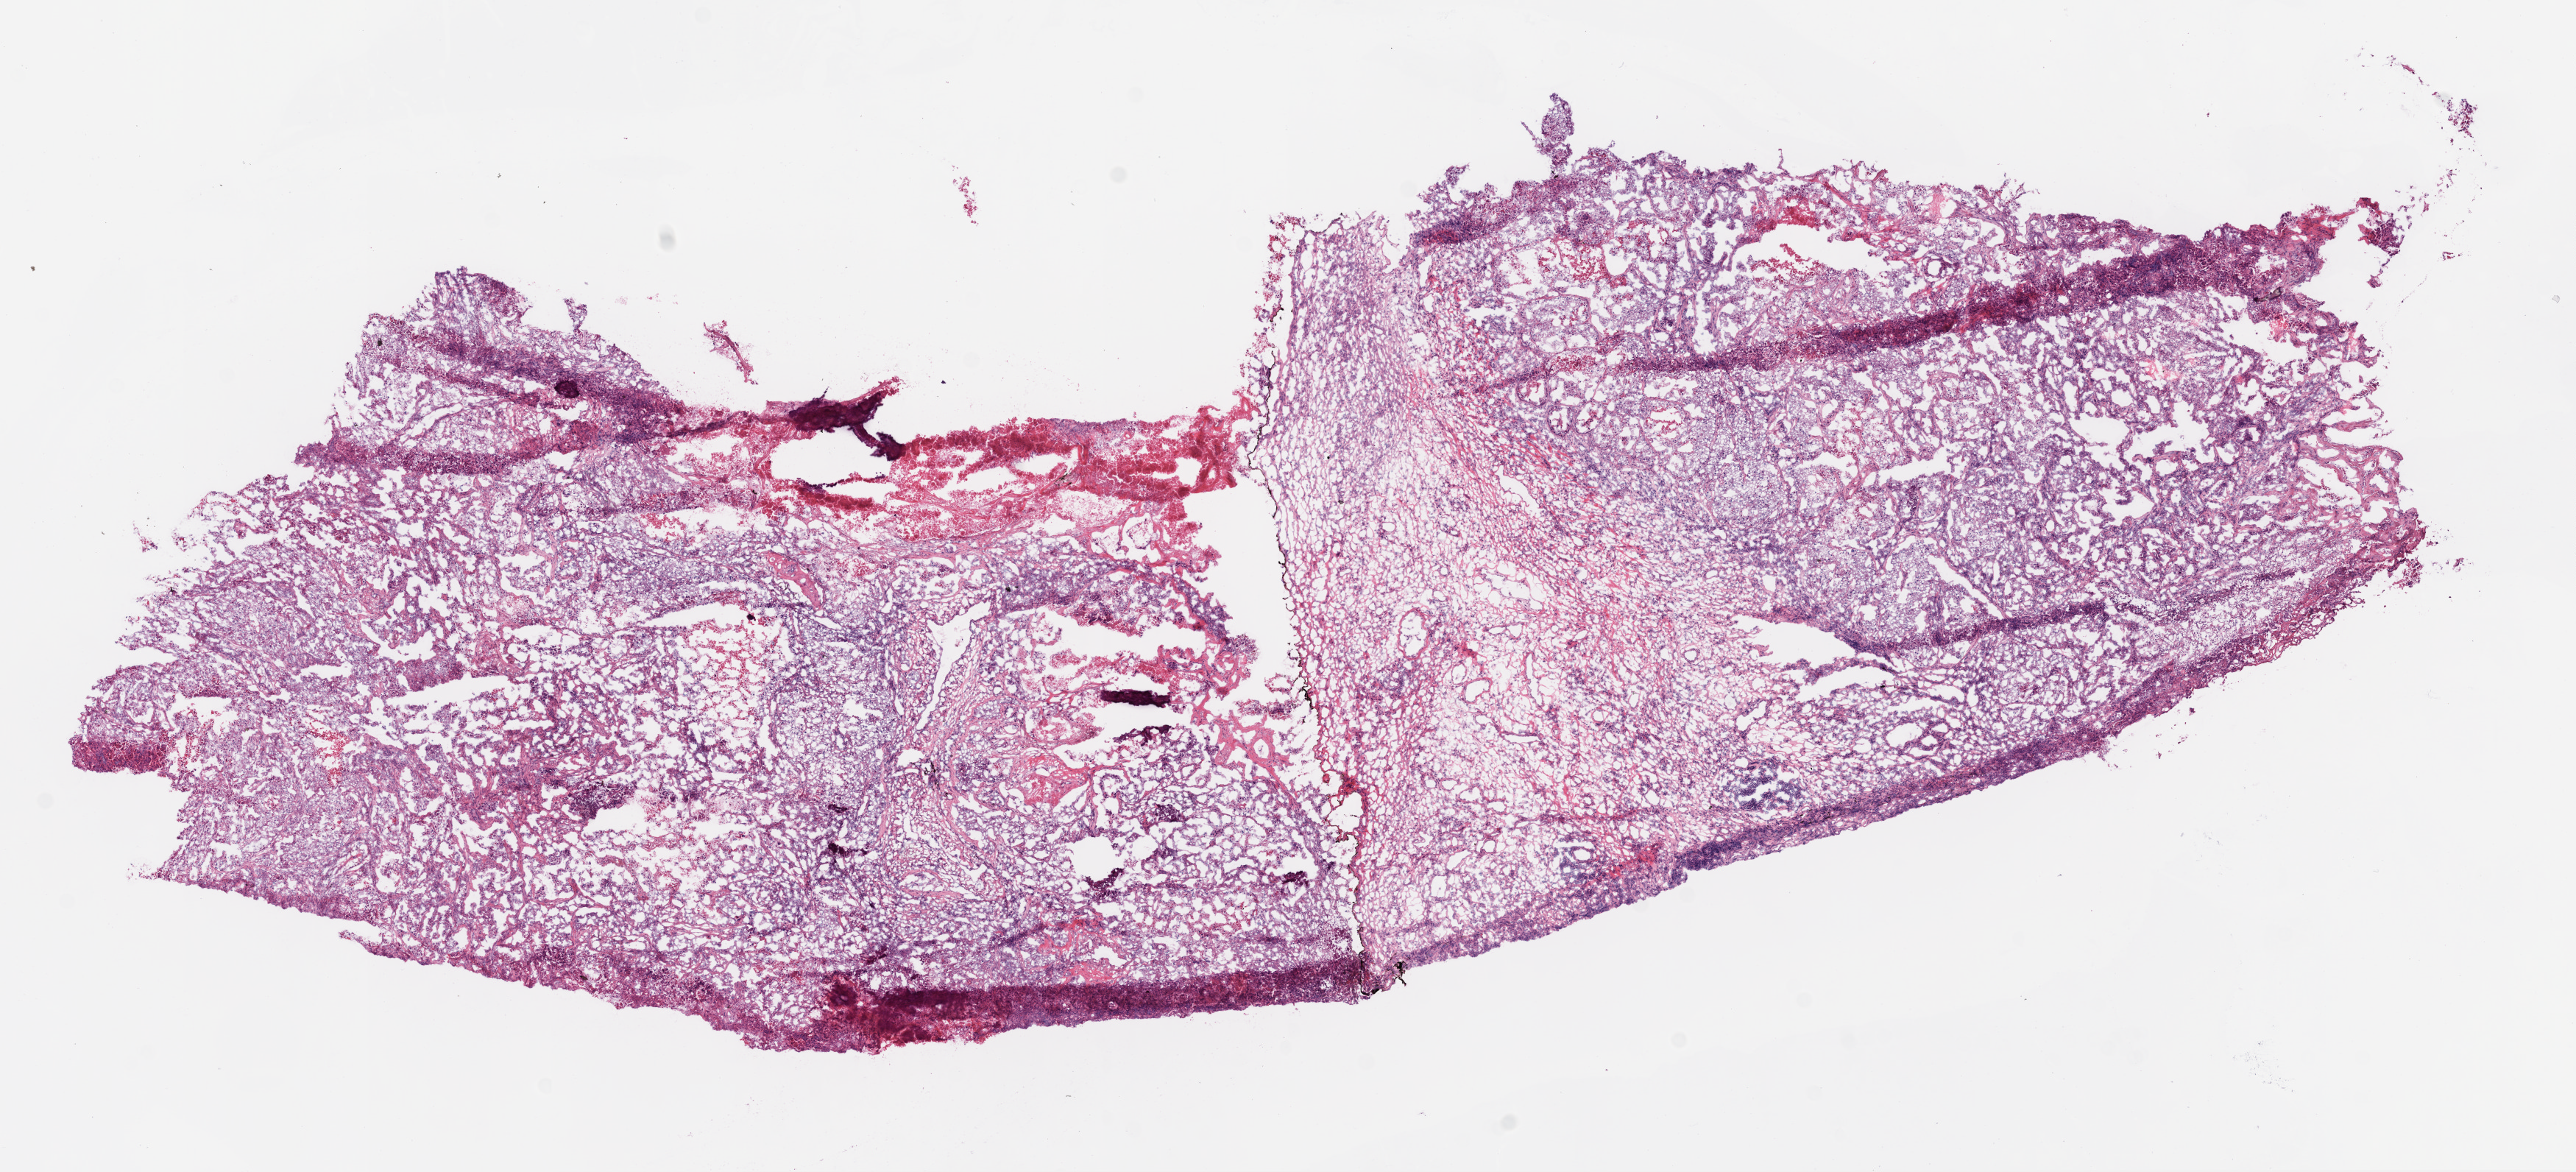
Whole-slide histology image, H&E — a low-resolution overview of the entire scanned area, about 14.0 x 6.4 mm (slide scanned at 20x). Frozen section from the bottom of the tissue portion. Primary tumour sample from the lung. Patient: female, age at initial diagnosis 62 years.
Histologic diagnosis: Squamous cell carcinoma, NOS (upper lobe, lung).